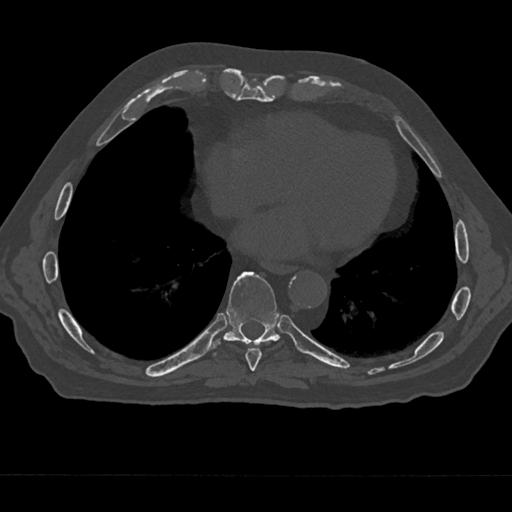
CT including the spine, one axial slice. Position 284 of 797 along the scan axis. Reconstruction kernel Br40s/3. Bone window (W 1800 / L 400 HU). 512 × 512 image matrix, field of view 377 × 377 mm. Patient: male, 75 years. From the clinical record (not read from this slice): primary cancer: renal.
Structures marked on this image (semi-automatically segmented with operator editing):
- T8 vertebra: bounding box <245,348,262,371> (left, top, right, bottom; pixels)
- T9 vertebra: <210,271,288,354>